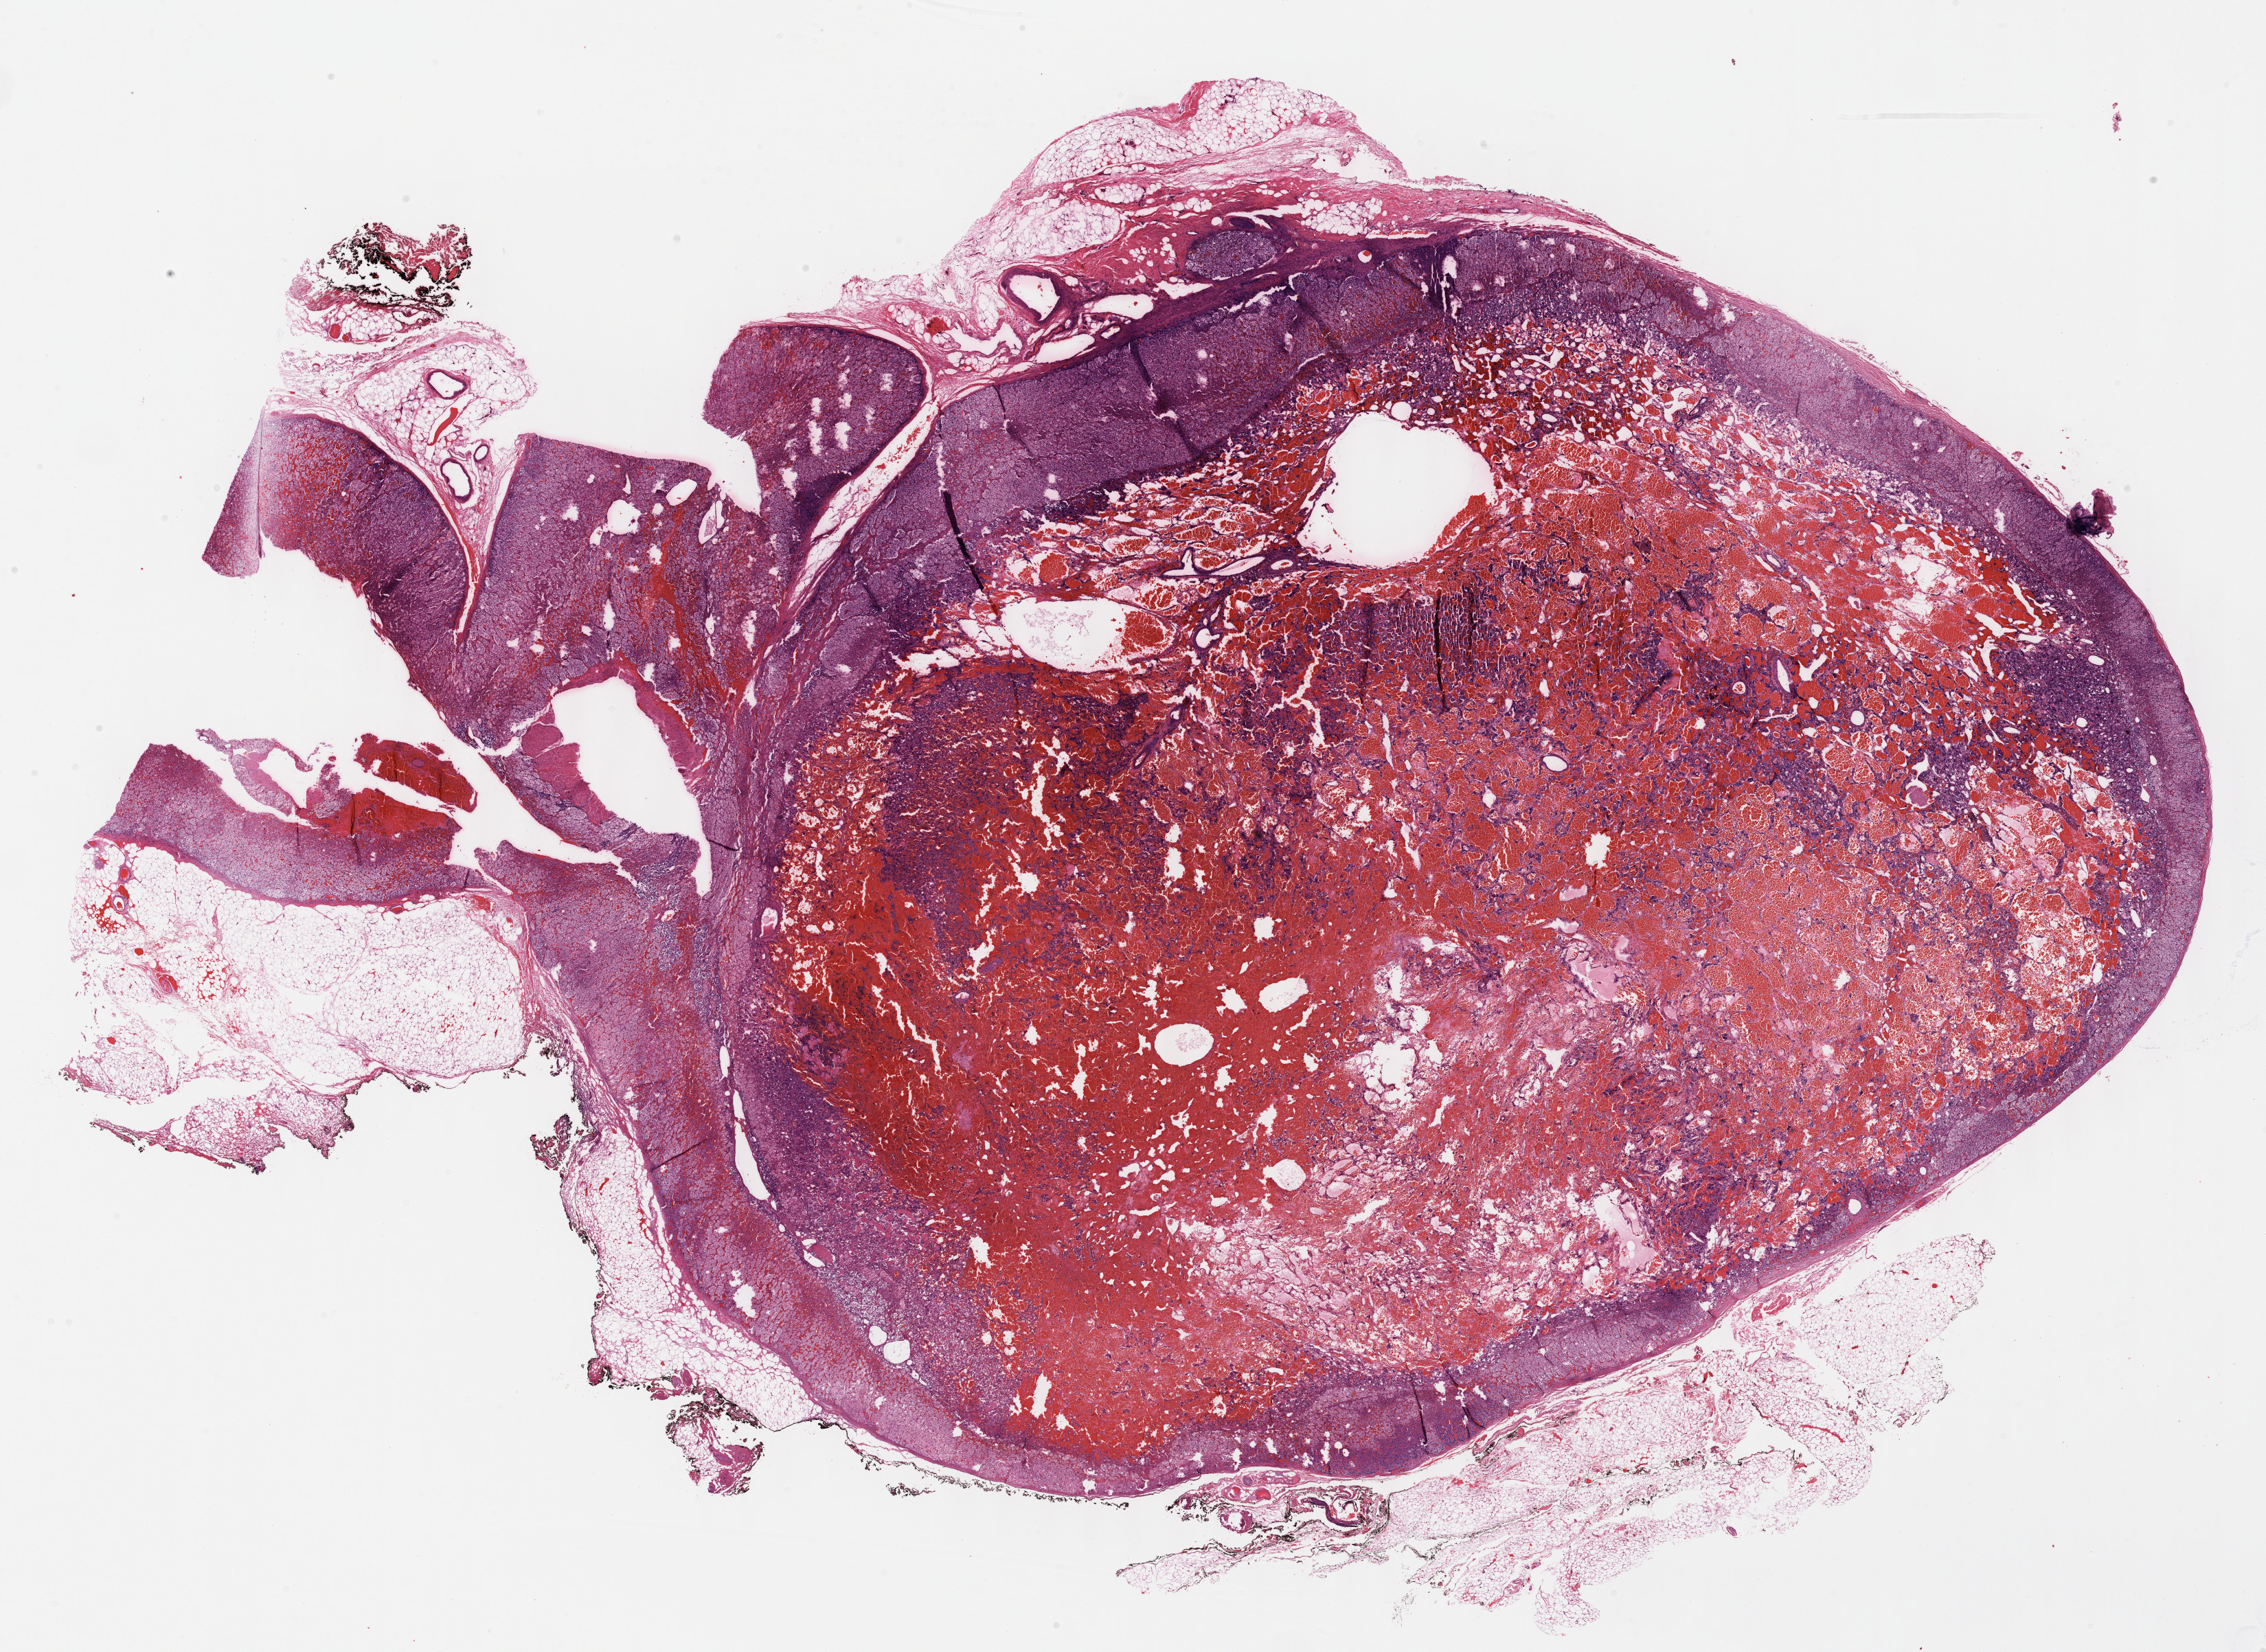
Whole-slide histology image, H&E, a low-resolution overview of the entire scanned area, about 26.7 x 19.4 mm (from a 40x scan), formalin-fixed paraffin-embedded (FFPE) diagnostic section, primary tumour sample from the adrenal gland. Female, age 64 years at initial diagnosis.
Histologic diagnosis: Pheochromocytoma, malignant.